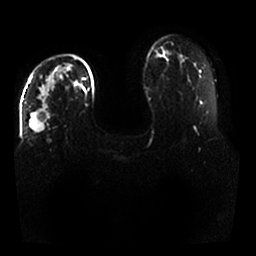
Breast MRI, one axial slice. Slice 19 of 25 in the series (ordered by position). Diffusion-weighted series; image 2 of 4 stored at this slice position (different b-values; order by instance number). 1.5 T. 4 mm slice thickness. 256 × 256 image matrix, field of view 350 × 350 mm. Female patient.
Structures marked on this image (outlined manually by an expert reader):
- tumour on diffusion-weighted imaging: box from (x=30, y=66) to (x=65, y=132) px